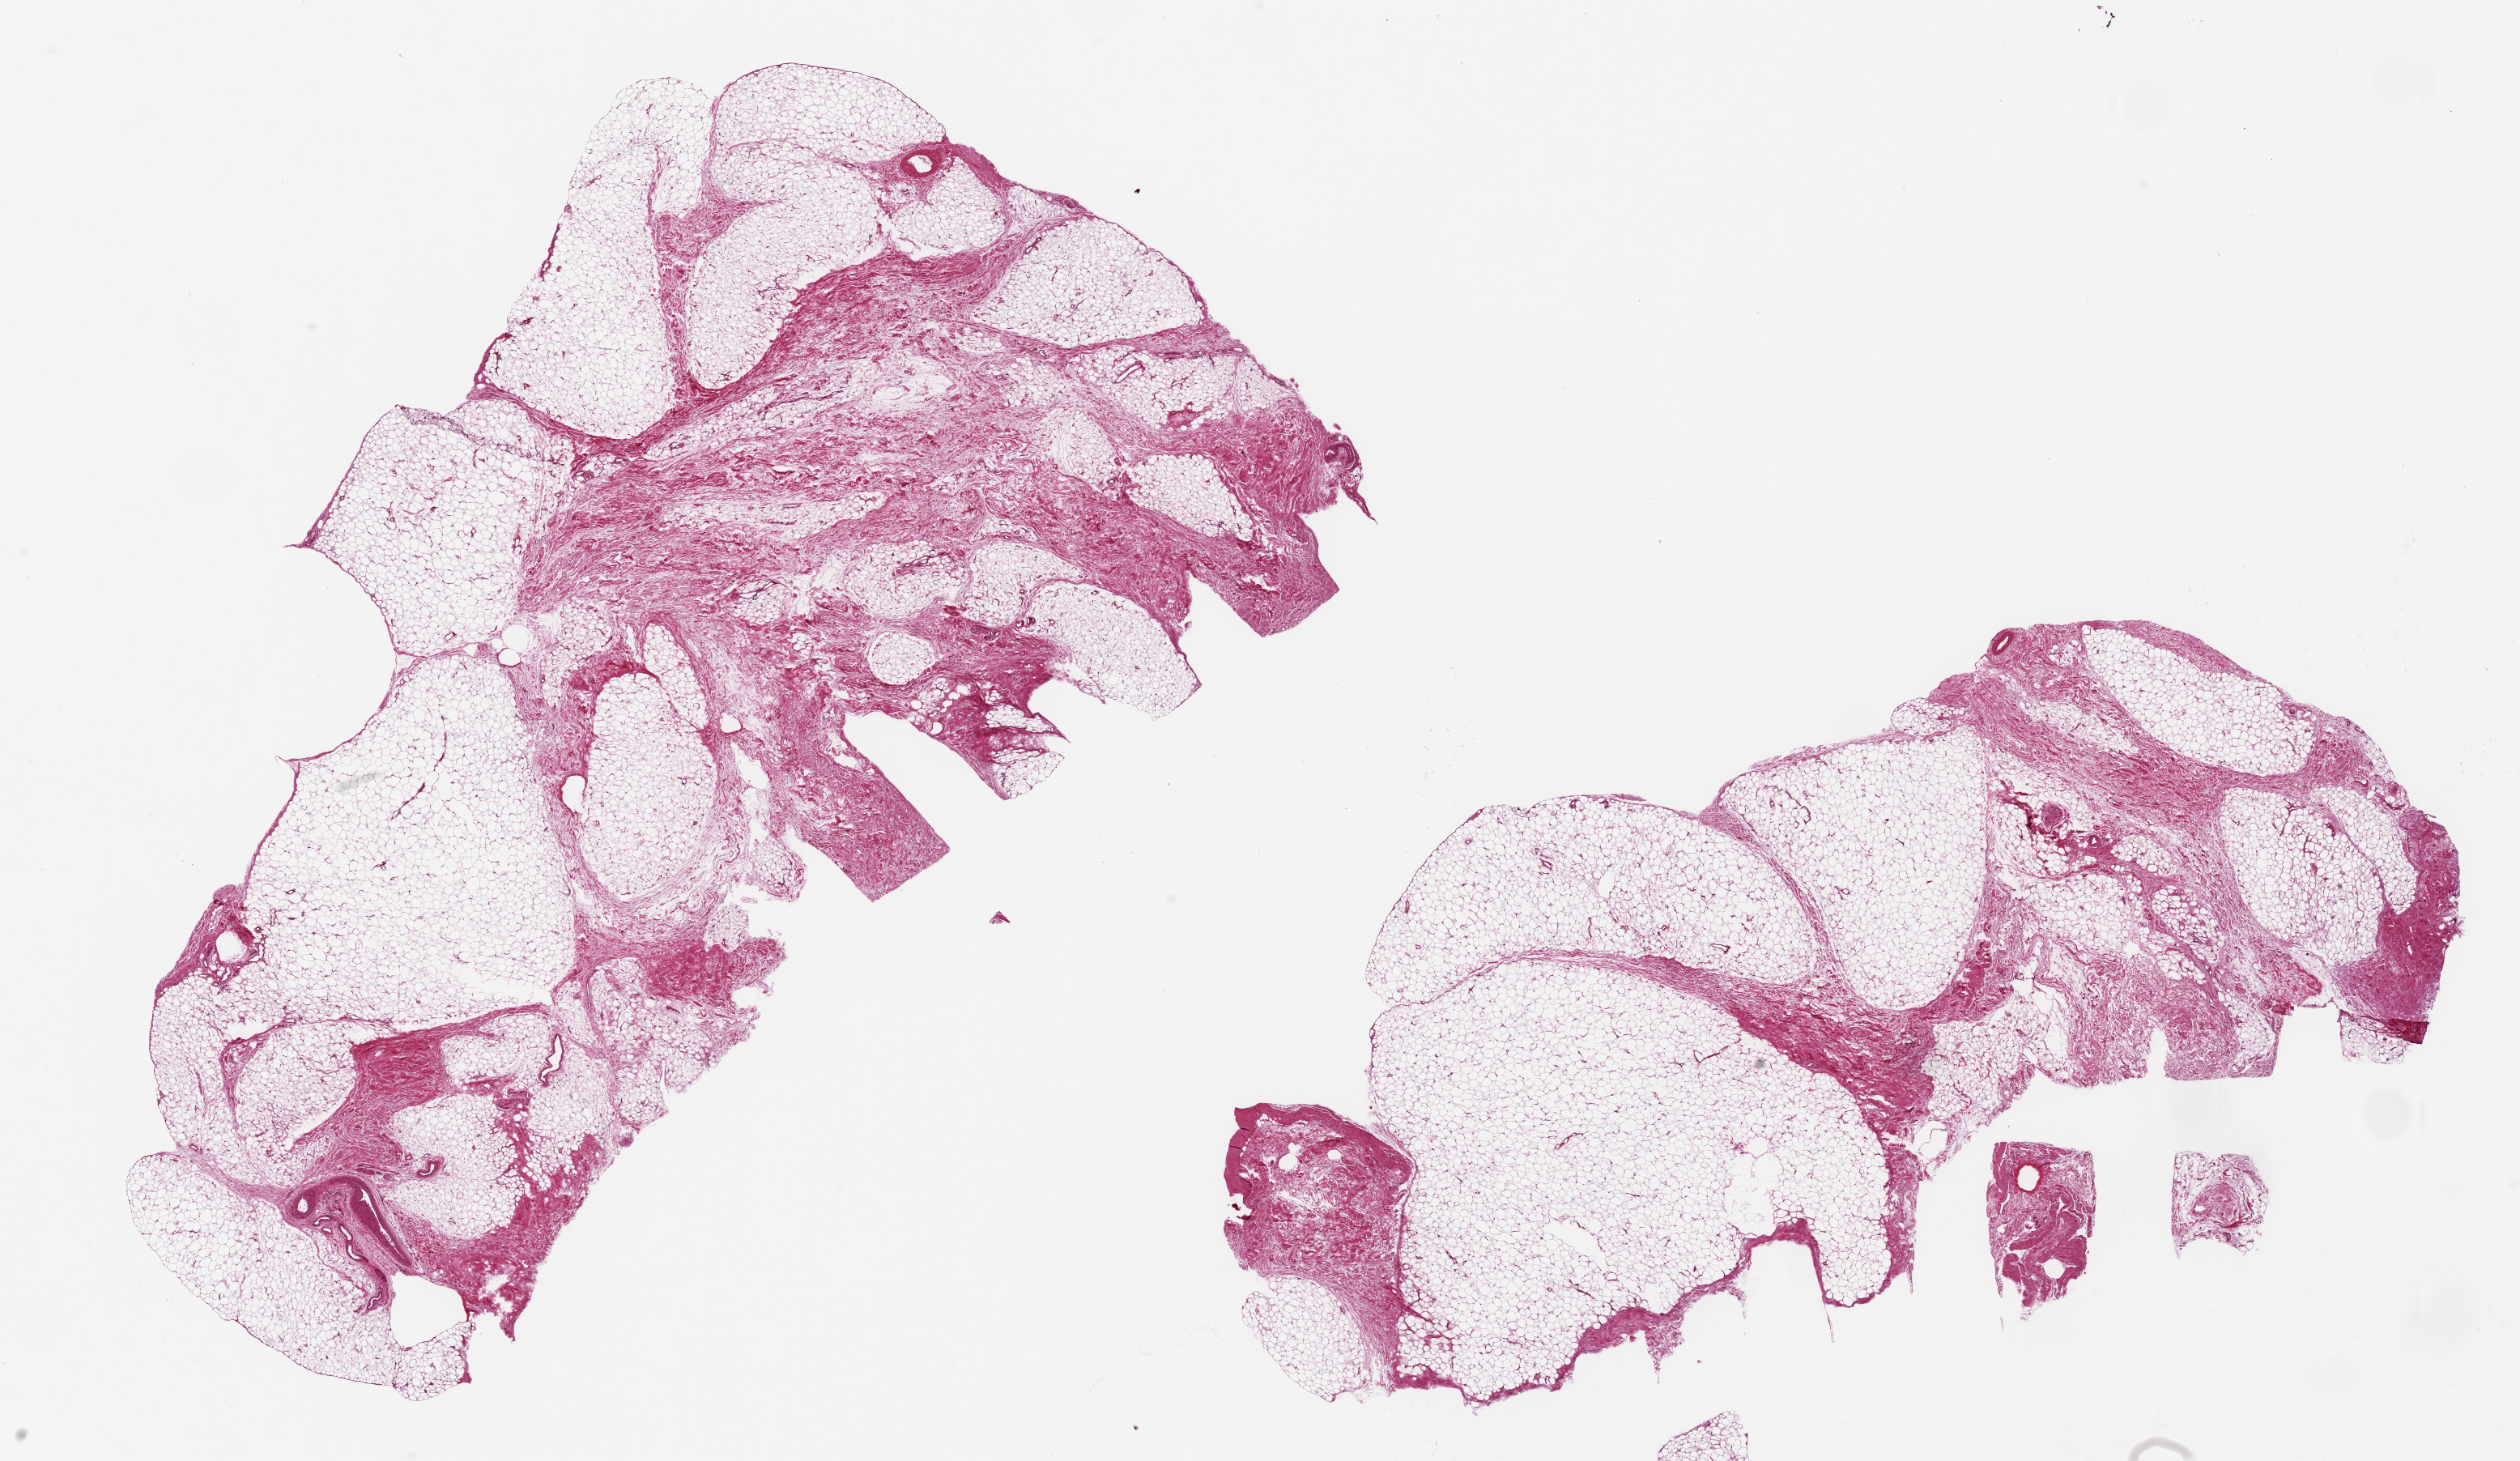
Digitized H&E-stained section — low-resolution overview of the scanned area, about 24.6 x 14.3 mm (slide scanned at 20x), PAXgene-fixed paraffin-embedded (PFPE) section, sampled site (target tissue): adipose tissue, tissue donor sample. Donor: male.
Pathologist's review note for this sample: 2 pieces 13x7 & 12x5 mm; 20-30% loose fibrous component.